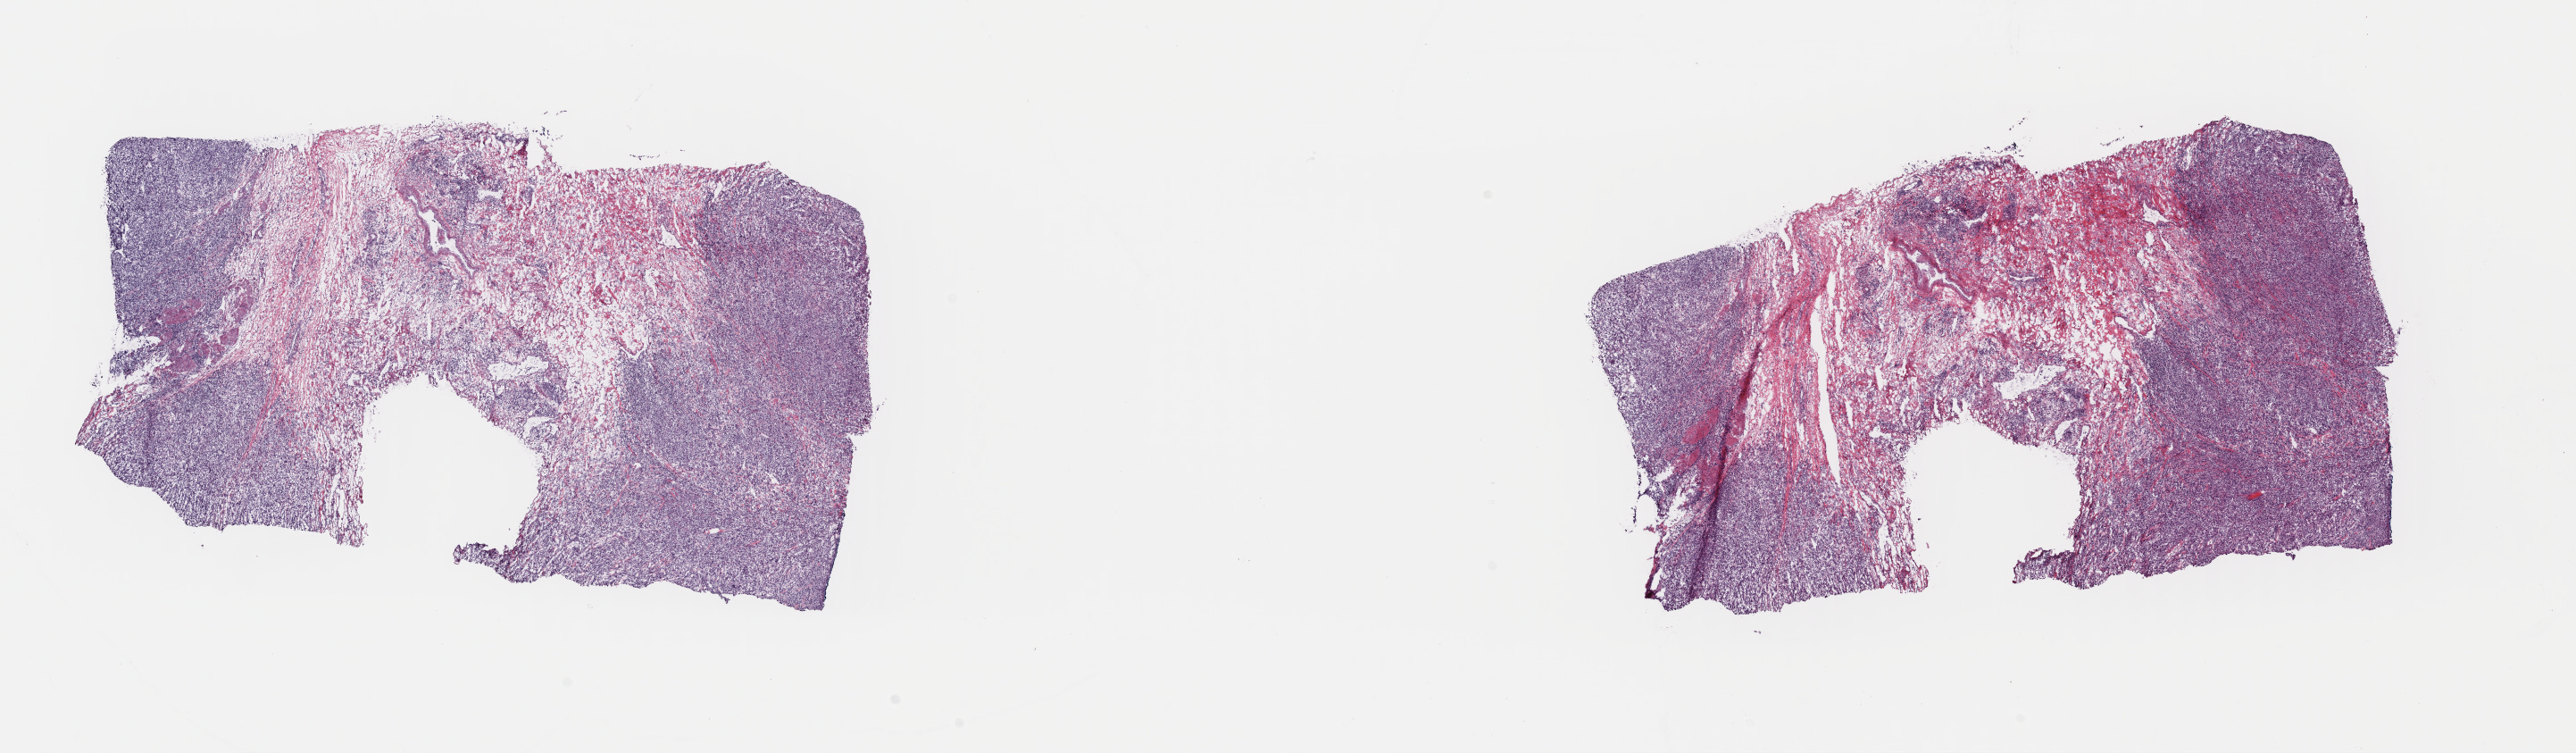
Digitized Hematoxylin and eosin (H&E) stained tissue section (whole slide), low-resolution overview of the scanned area, about 22.7 x 6.6 mm; frozen section; primary tumour sample from the bladder. Male patient; age at initial diagnosis 69 years. Histologic grade: high grade. Pathologist review of this section (percent, as recorded): tumour cells 35%, tumour nuclei 65%, normal cells 0%, stromal cells 63%, necrosis 2%. Infiltration values recorded for this section: lymphocyte infiltration 25%, monocyte infiltration 3%, neutrophil infiltration 3%.
Pathologic diagnosis: Transitional cell carcinoma (trigone of bladder). AJCC pathologic stage: III (7th edition).